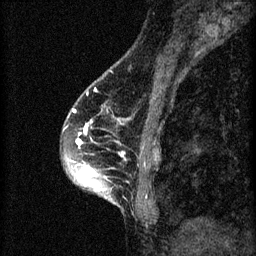
Breast MRI (dynamic contrast-enhanced), one sagittal slice. Slice 23 of 60 in the series (ordered by position). 3 images stored at this slice position (order not interpretable as contrast timing). 1.5 T. TE 4.2 ms, TR 8.2 ms. 2 mm slice thickness. 256 × 256 image matrix, field of view 180 × 180 mm. Female patient, age 45 years.
Structures marked on this image (semi-automatic segmentation, software-assisted and operator-edited):
- analysis volume of interest (the breast-tissue region the enhancement analysis was run in; not a lesion): bounding box [x1, y1, x2, y2] px = [62, 104, 159, 217]
- tumour enhancement mask (voxels above the 70 % enhancement threshold inside the analysis volume of interest): [72, 110, 125, 201]